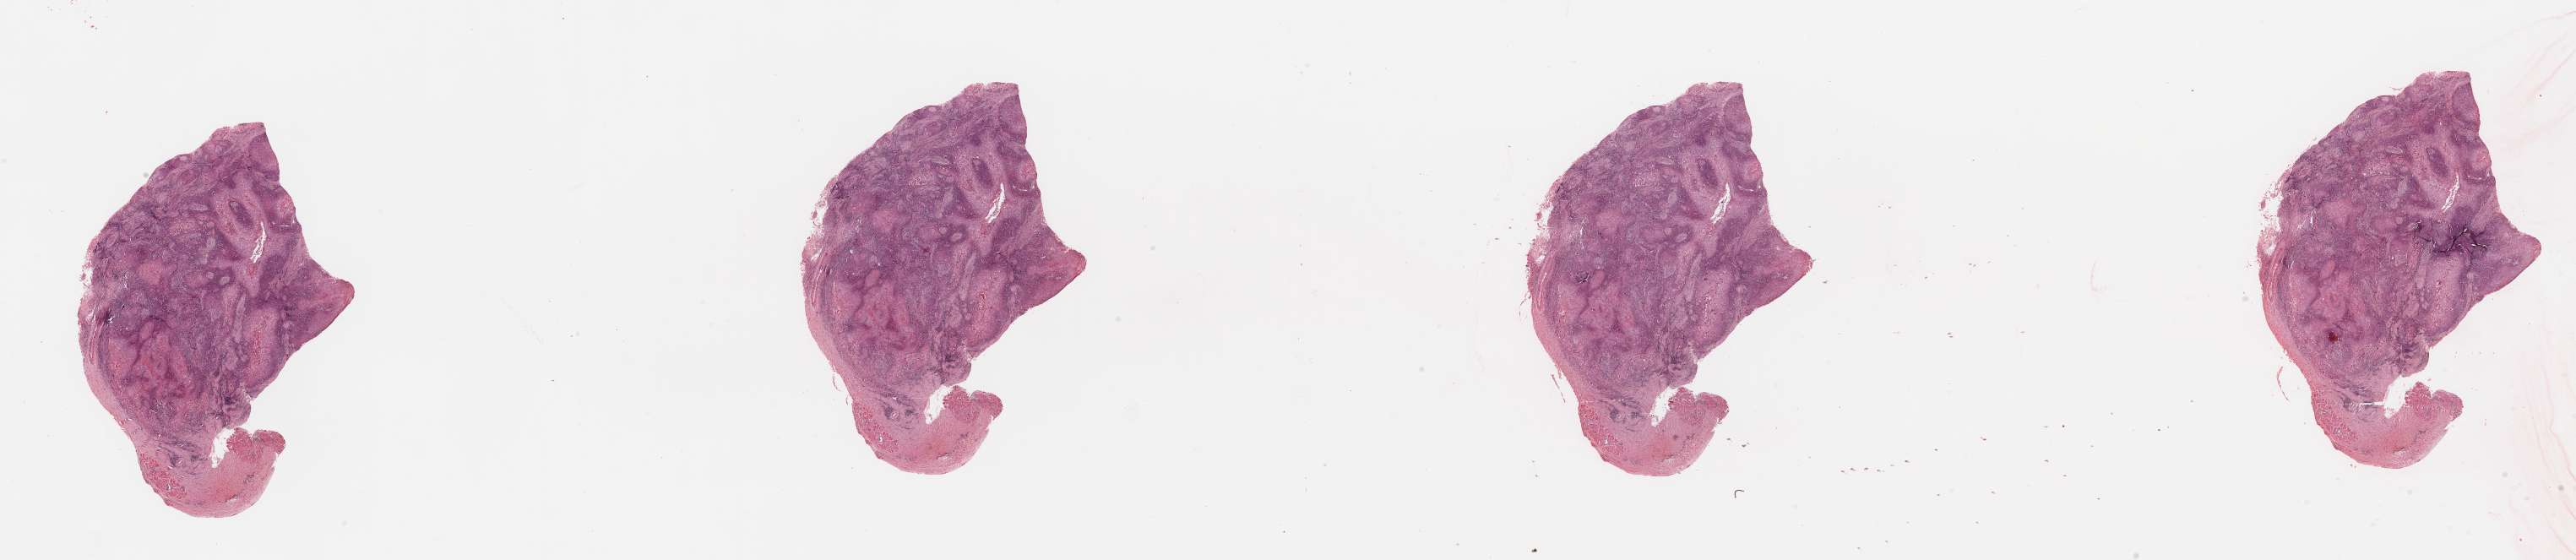
Whole-slide histology image, Hematoxylin and eosin (H&E) stained — a low-resolution overview of the entire scanned area, about 48.2 x 10.5 mm (from a 20x scan), tumour tissue sample, sampled site: larynx. 81-year-old male patient. Histologic grade: G2 (moderately differentiated). Composition of this section per pathologist review: tumour nuclei 85%, necrosis 5%.
AJCC pathologic stage: II. Histologic diagnosis: Squamous cell carcinoma, NOS (larynx, NOS).